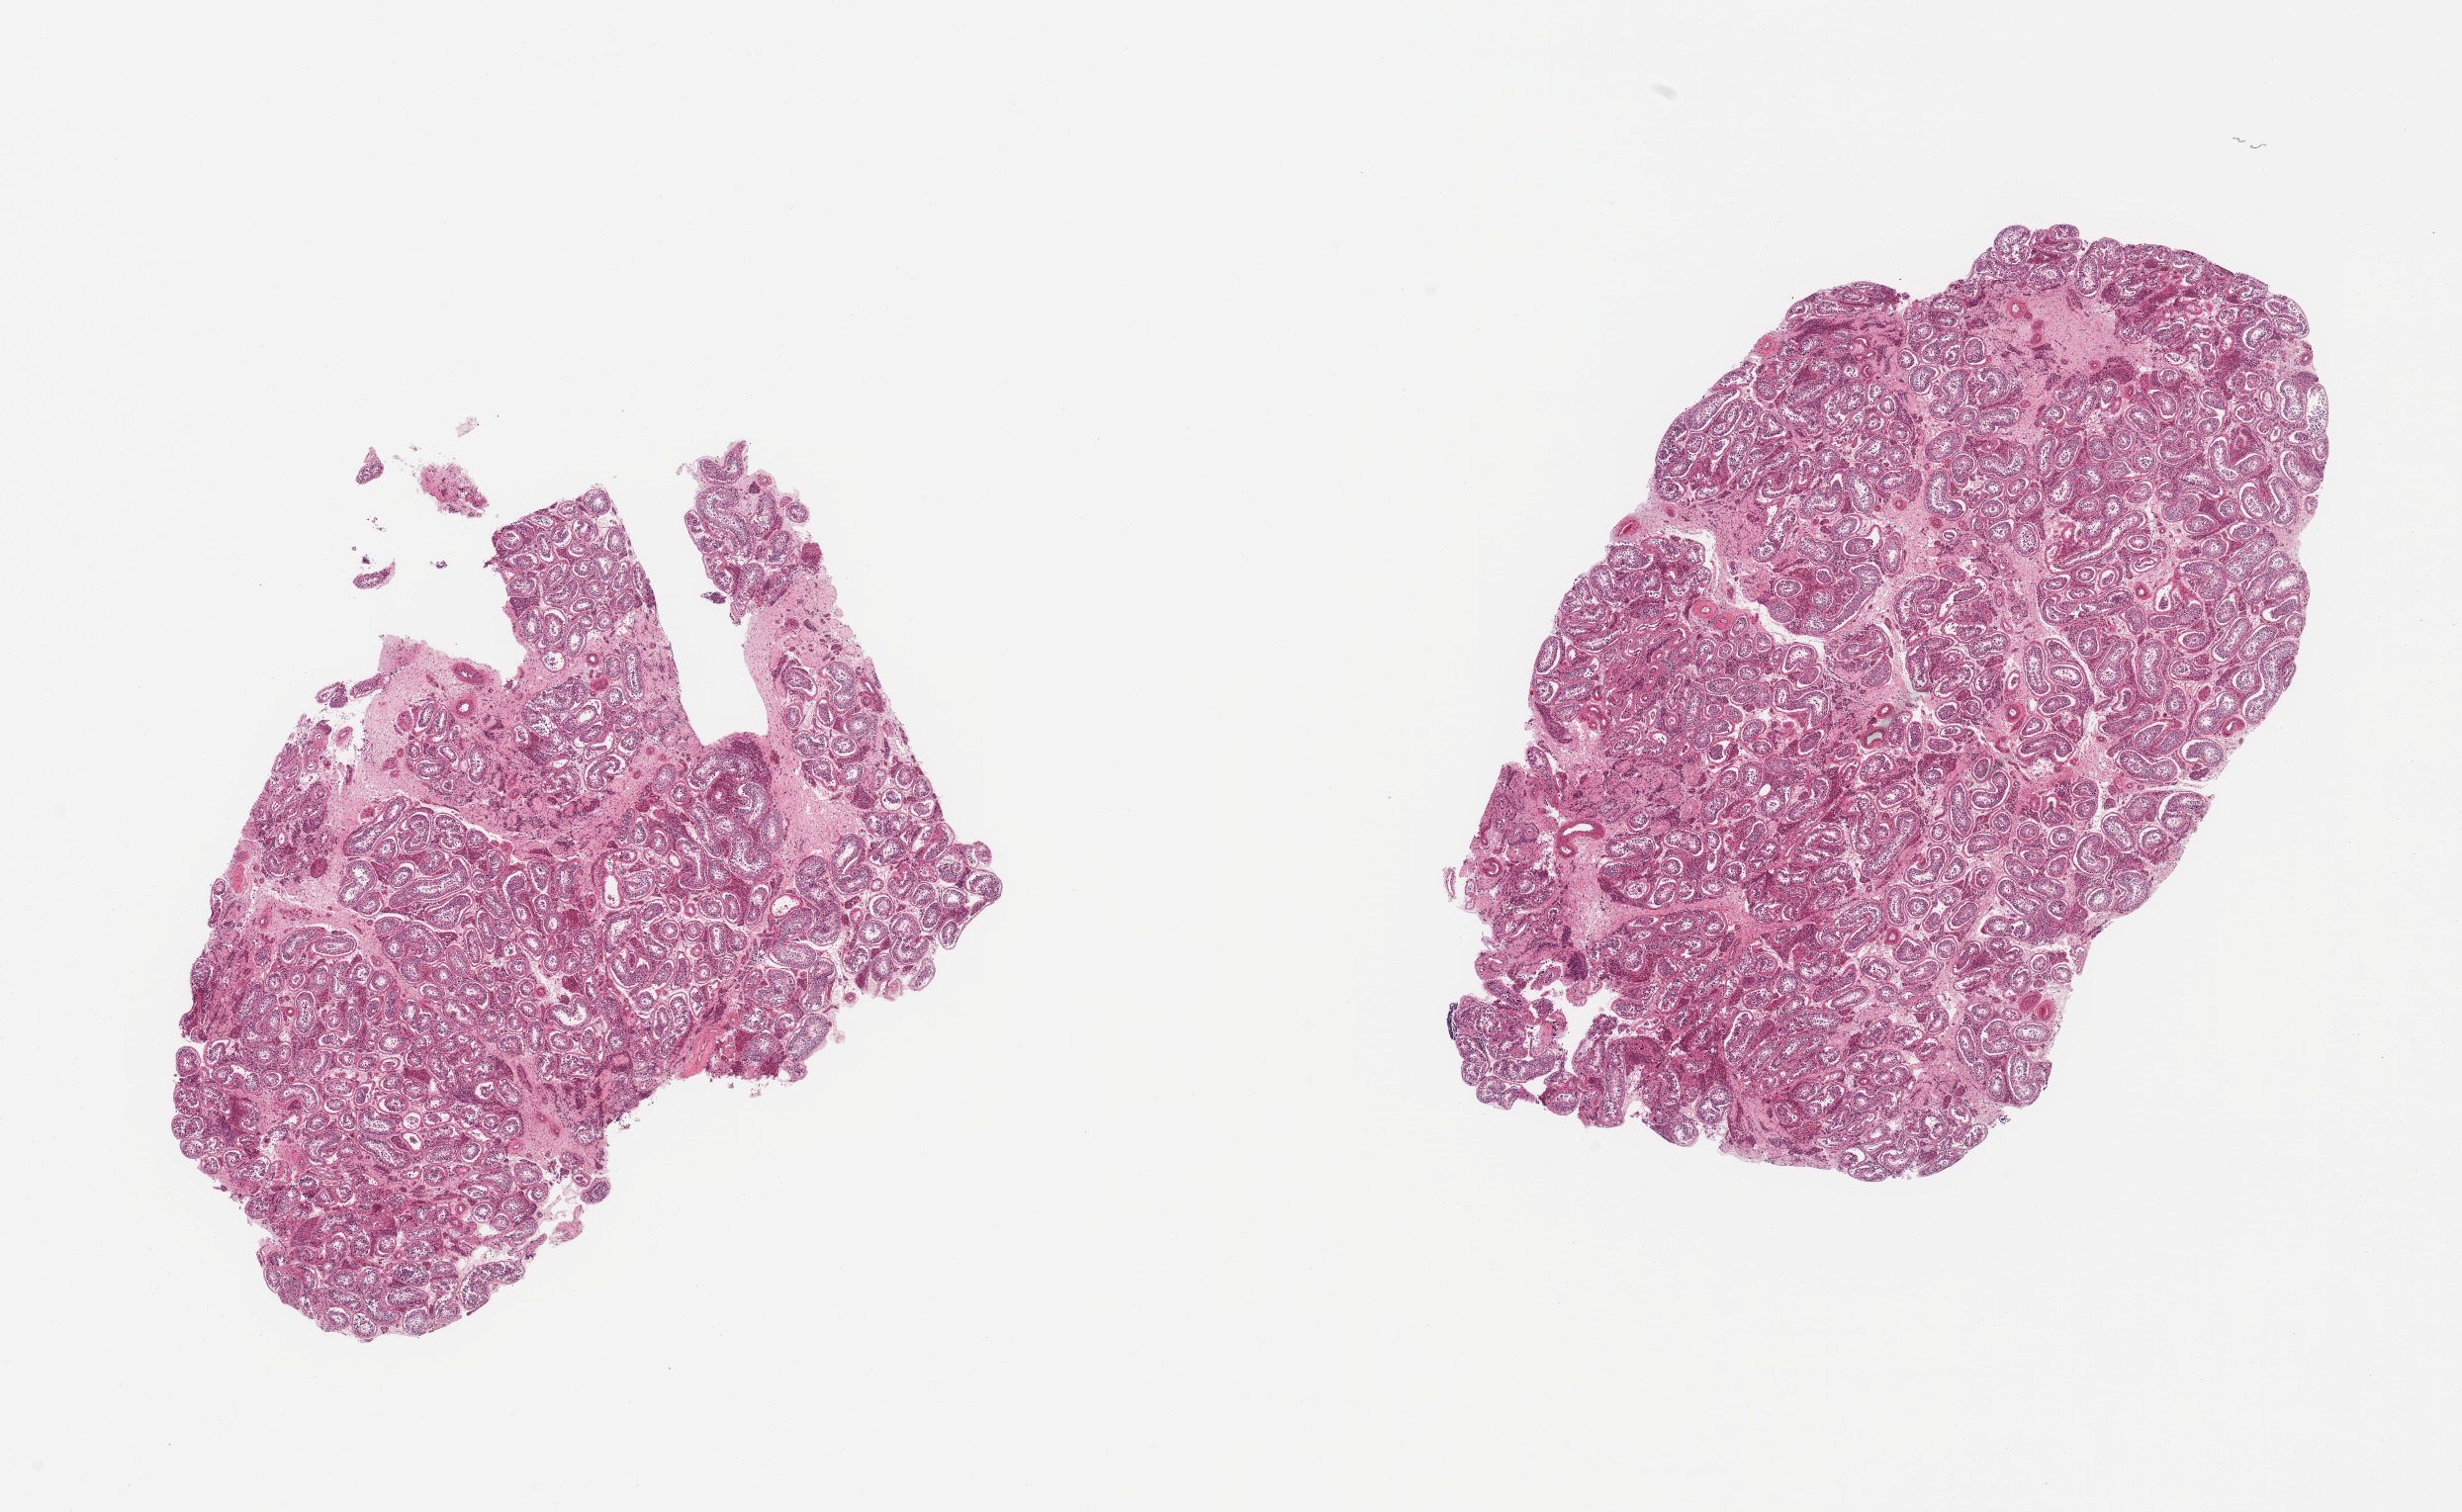
Digitized hematoxylin and eosin (H&E)-stained section — a low-resolution overview of the entire scanned area, about 19.7 x 12.1 mm (from a 20x scan), PAXgene-fixed paraffin-embedded (PFPE) section, target tissue: testis, tissue donor sample. Donor sex: male.
Pathologist's review note for this sample: 2 pieces; decreased spermatogenesis; interstitial fibrosis with tubular atrophy and sclerosis with interstitial proliferation of Leydig cells.